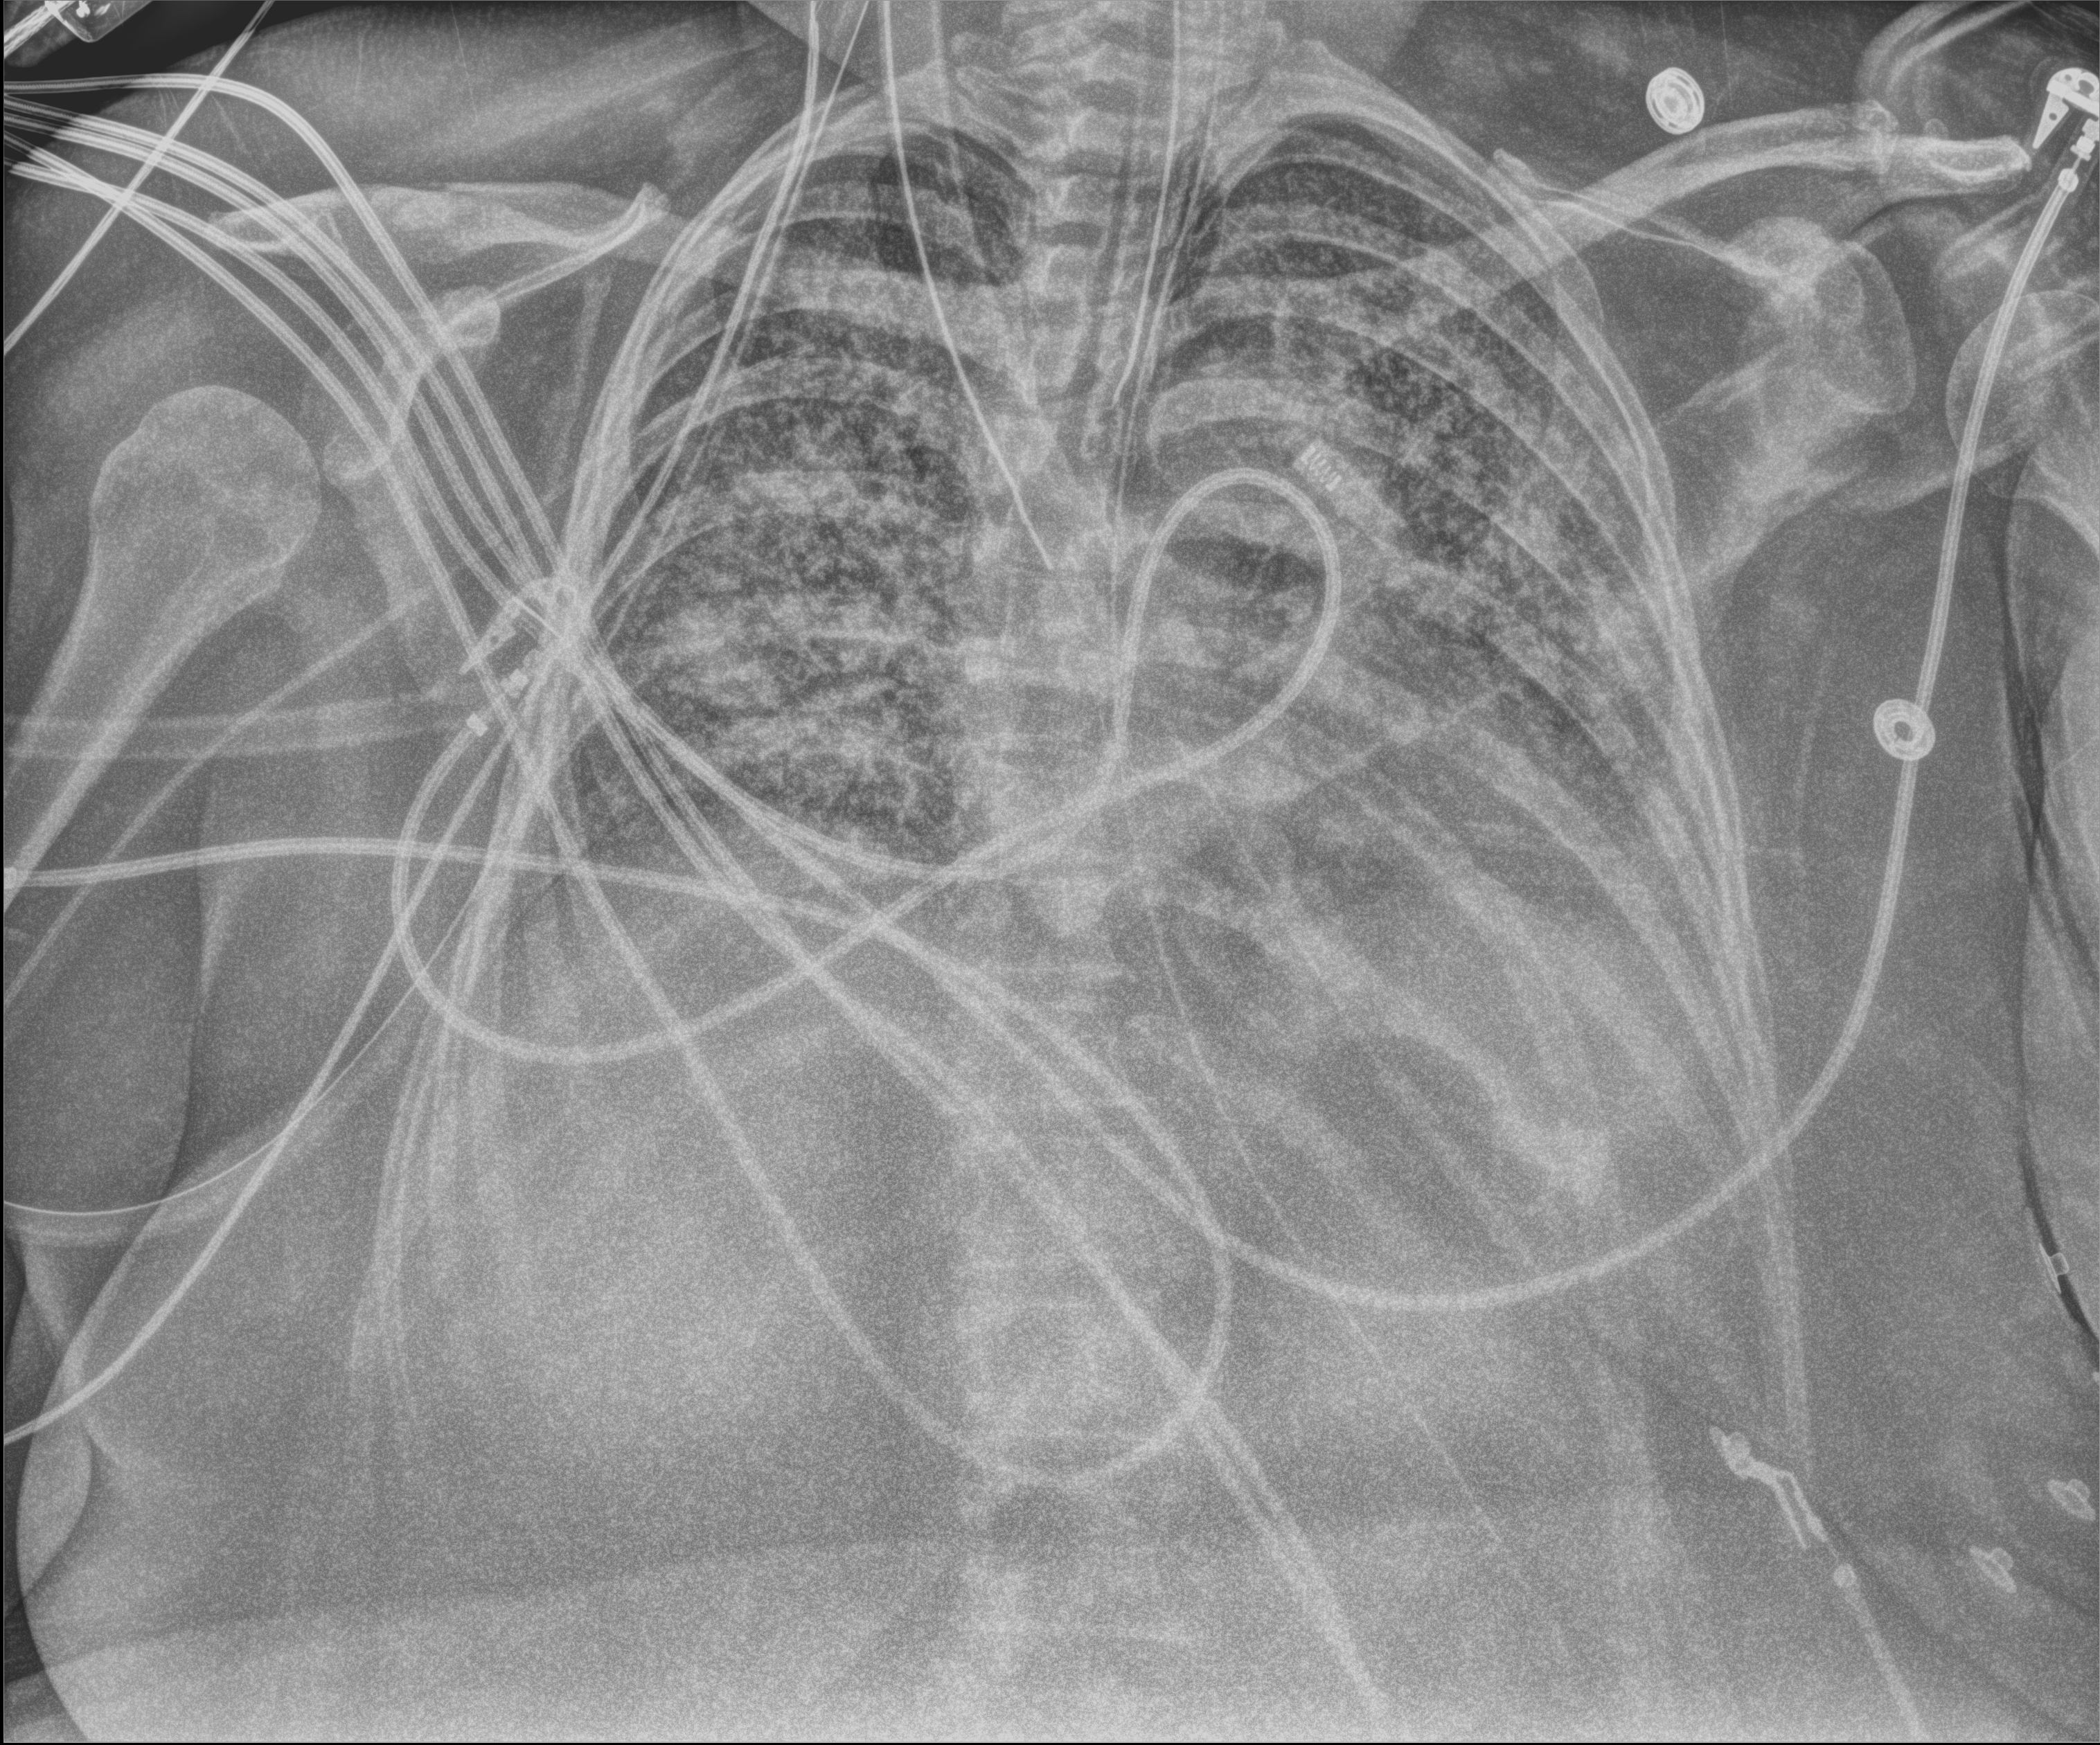
Portable chest radiograph, anteroposterior (AP) projection. Female patient hospitalised with COVID-19, age 18–59 years.
Hospital-stay facts (about this admission, not read from this image; timing relative to this image not recorded): mechanically ventilated during this hospital stay: yes; other chronic lung disease (admission record): no; chronic kidney disease (admission record): no.